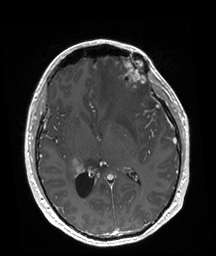
Brain MRI from a brain-tumour surgery series, one axial slice. Position 93 of 192 along the scan axis. T1-weighted post-contrast. 1 mm slice thickness. 216 × 256 image matrix.
Structures marked on this image (expert manual segmentation):
- tumour: bounding box <120,57,146,98> (left, top, right, bottom; pixels)